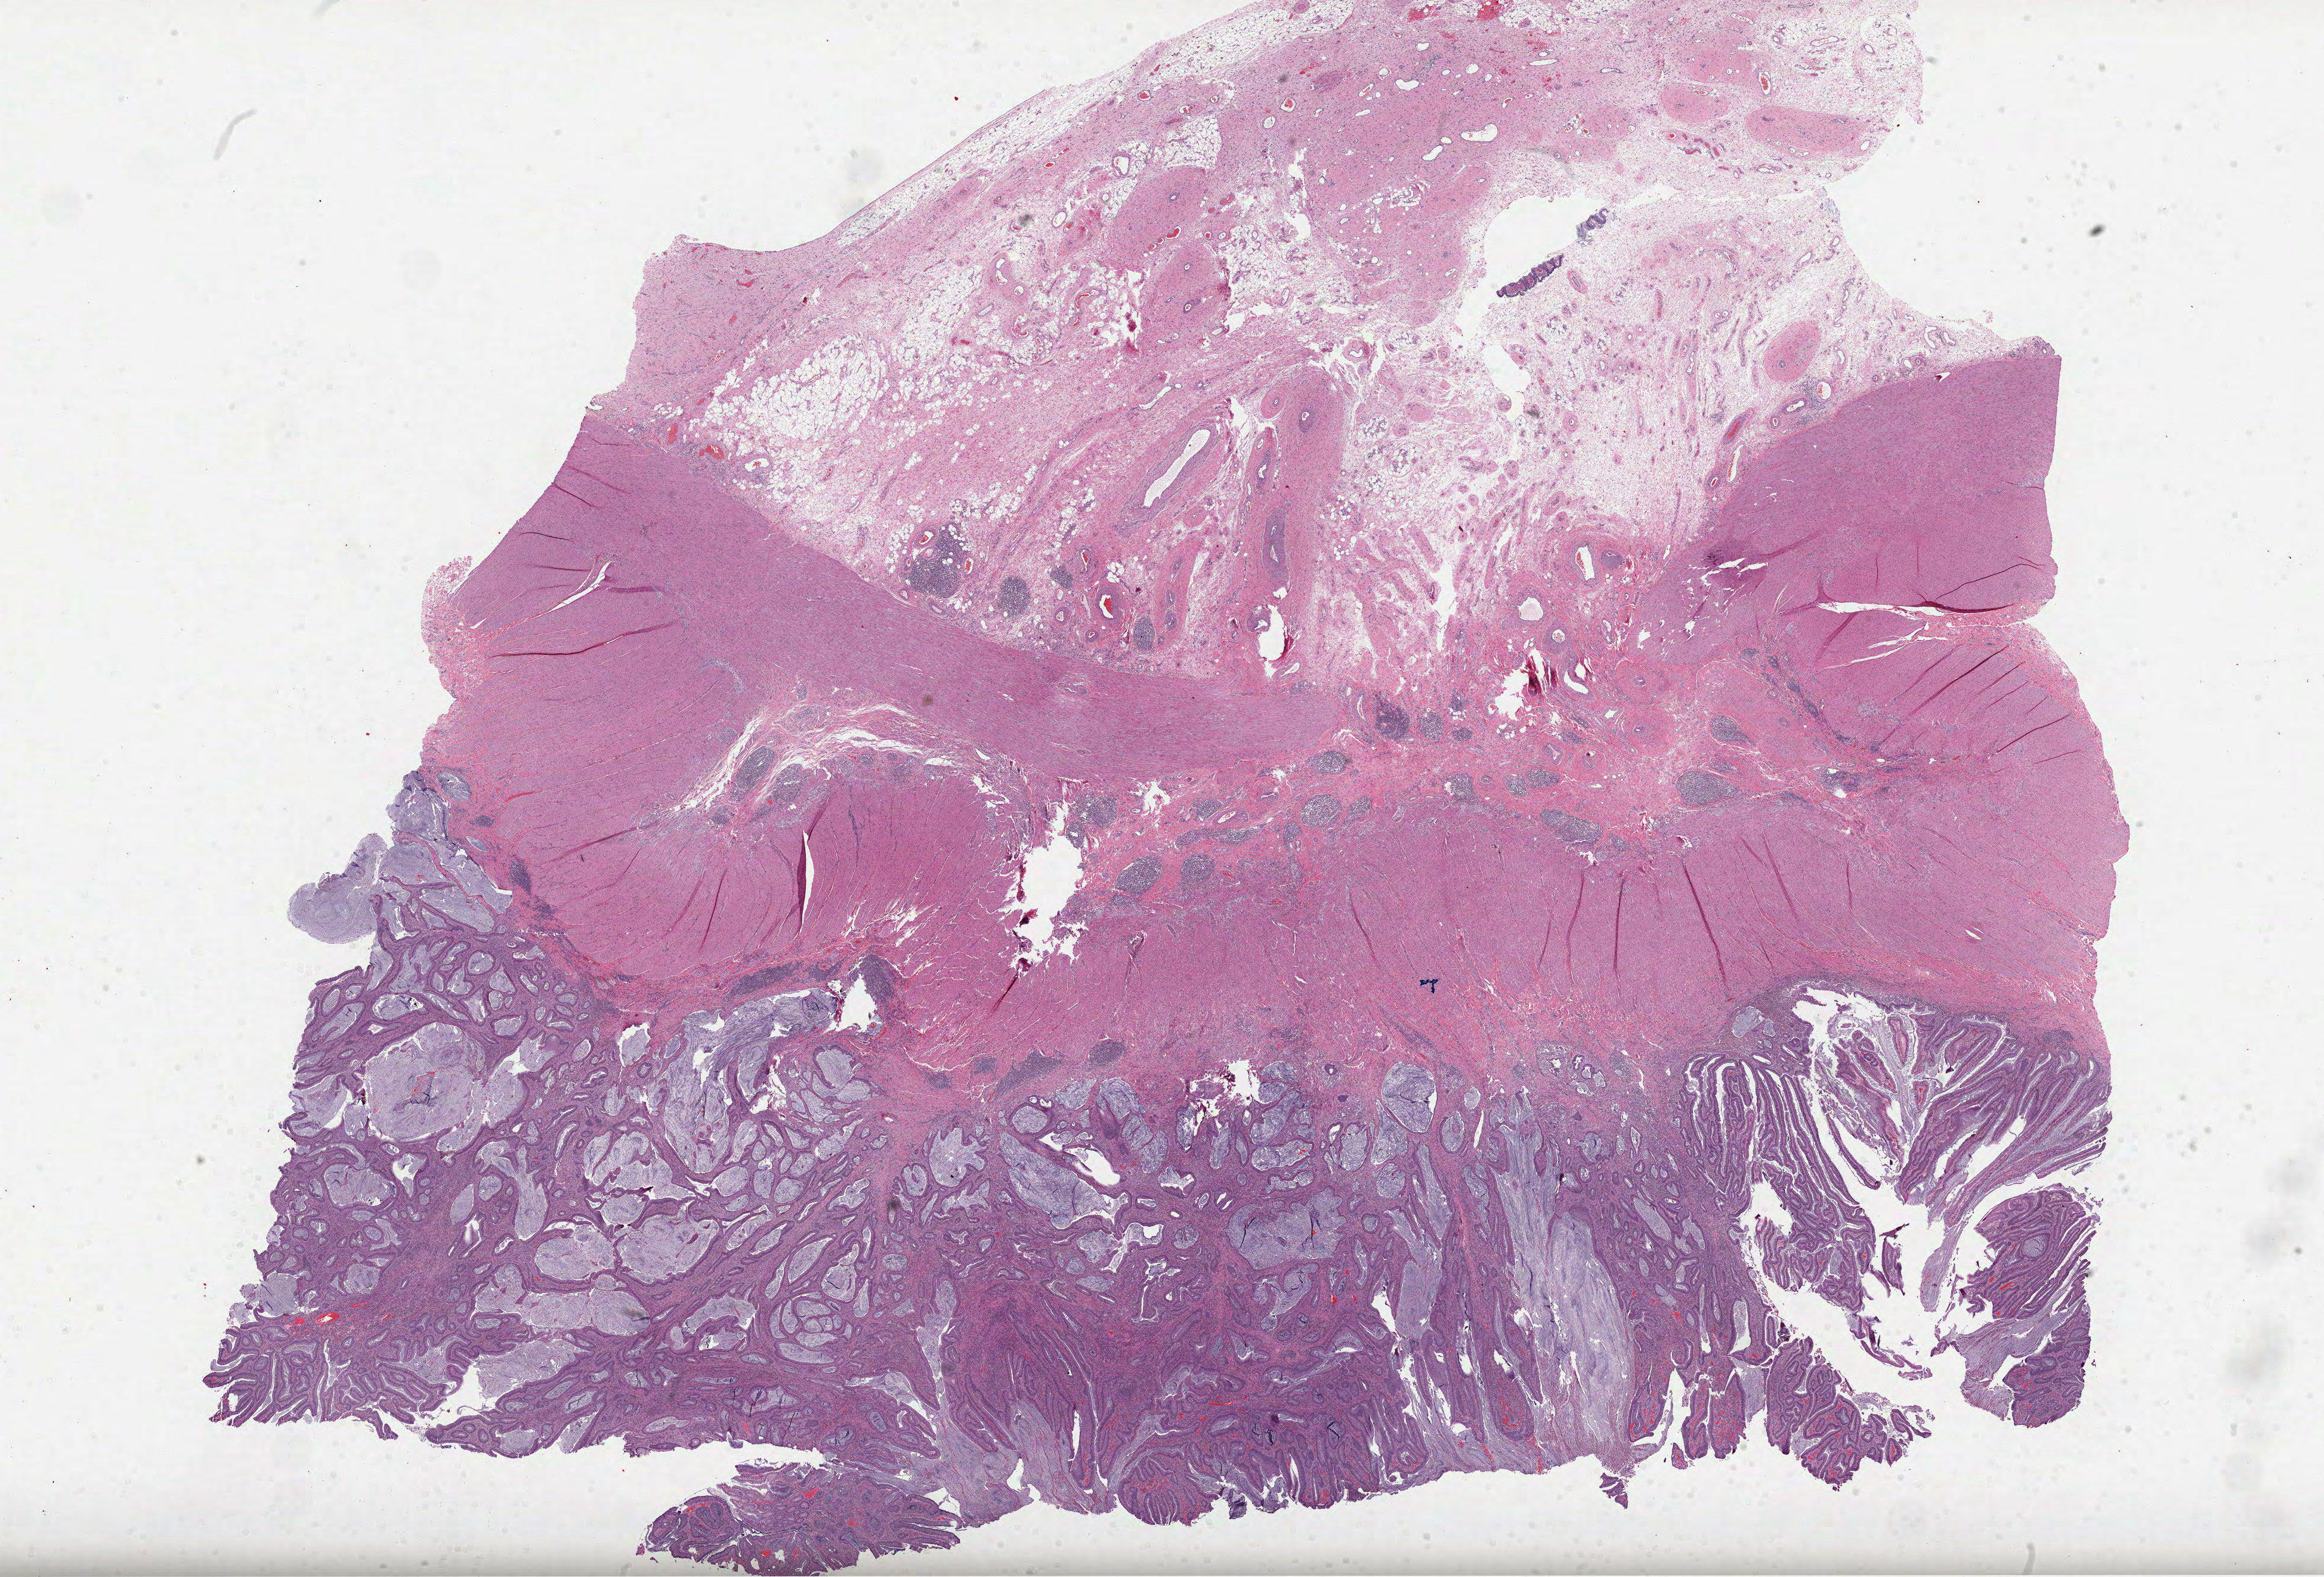
Hematoxylin and eosin (H&E) stained whole-slide image, low-resolution overview of the scanned area, about 31.4 x 21.3 mm (slide scanned at 40x). Formalin-fixed paraffin-embedded (FFPE) diagnostic section. Colon, primary tumour sample. Male patient; age at initial diagnosis 39 years.
- histologic diagnosis: Adenocarcinoma, NOS (hepatic flexure of colon)
- AJCC pathologic stage: IIA (7th edition)